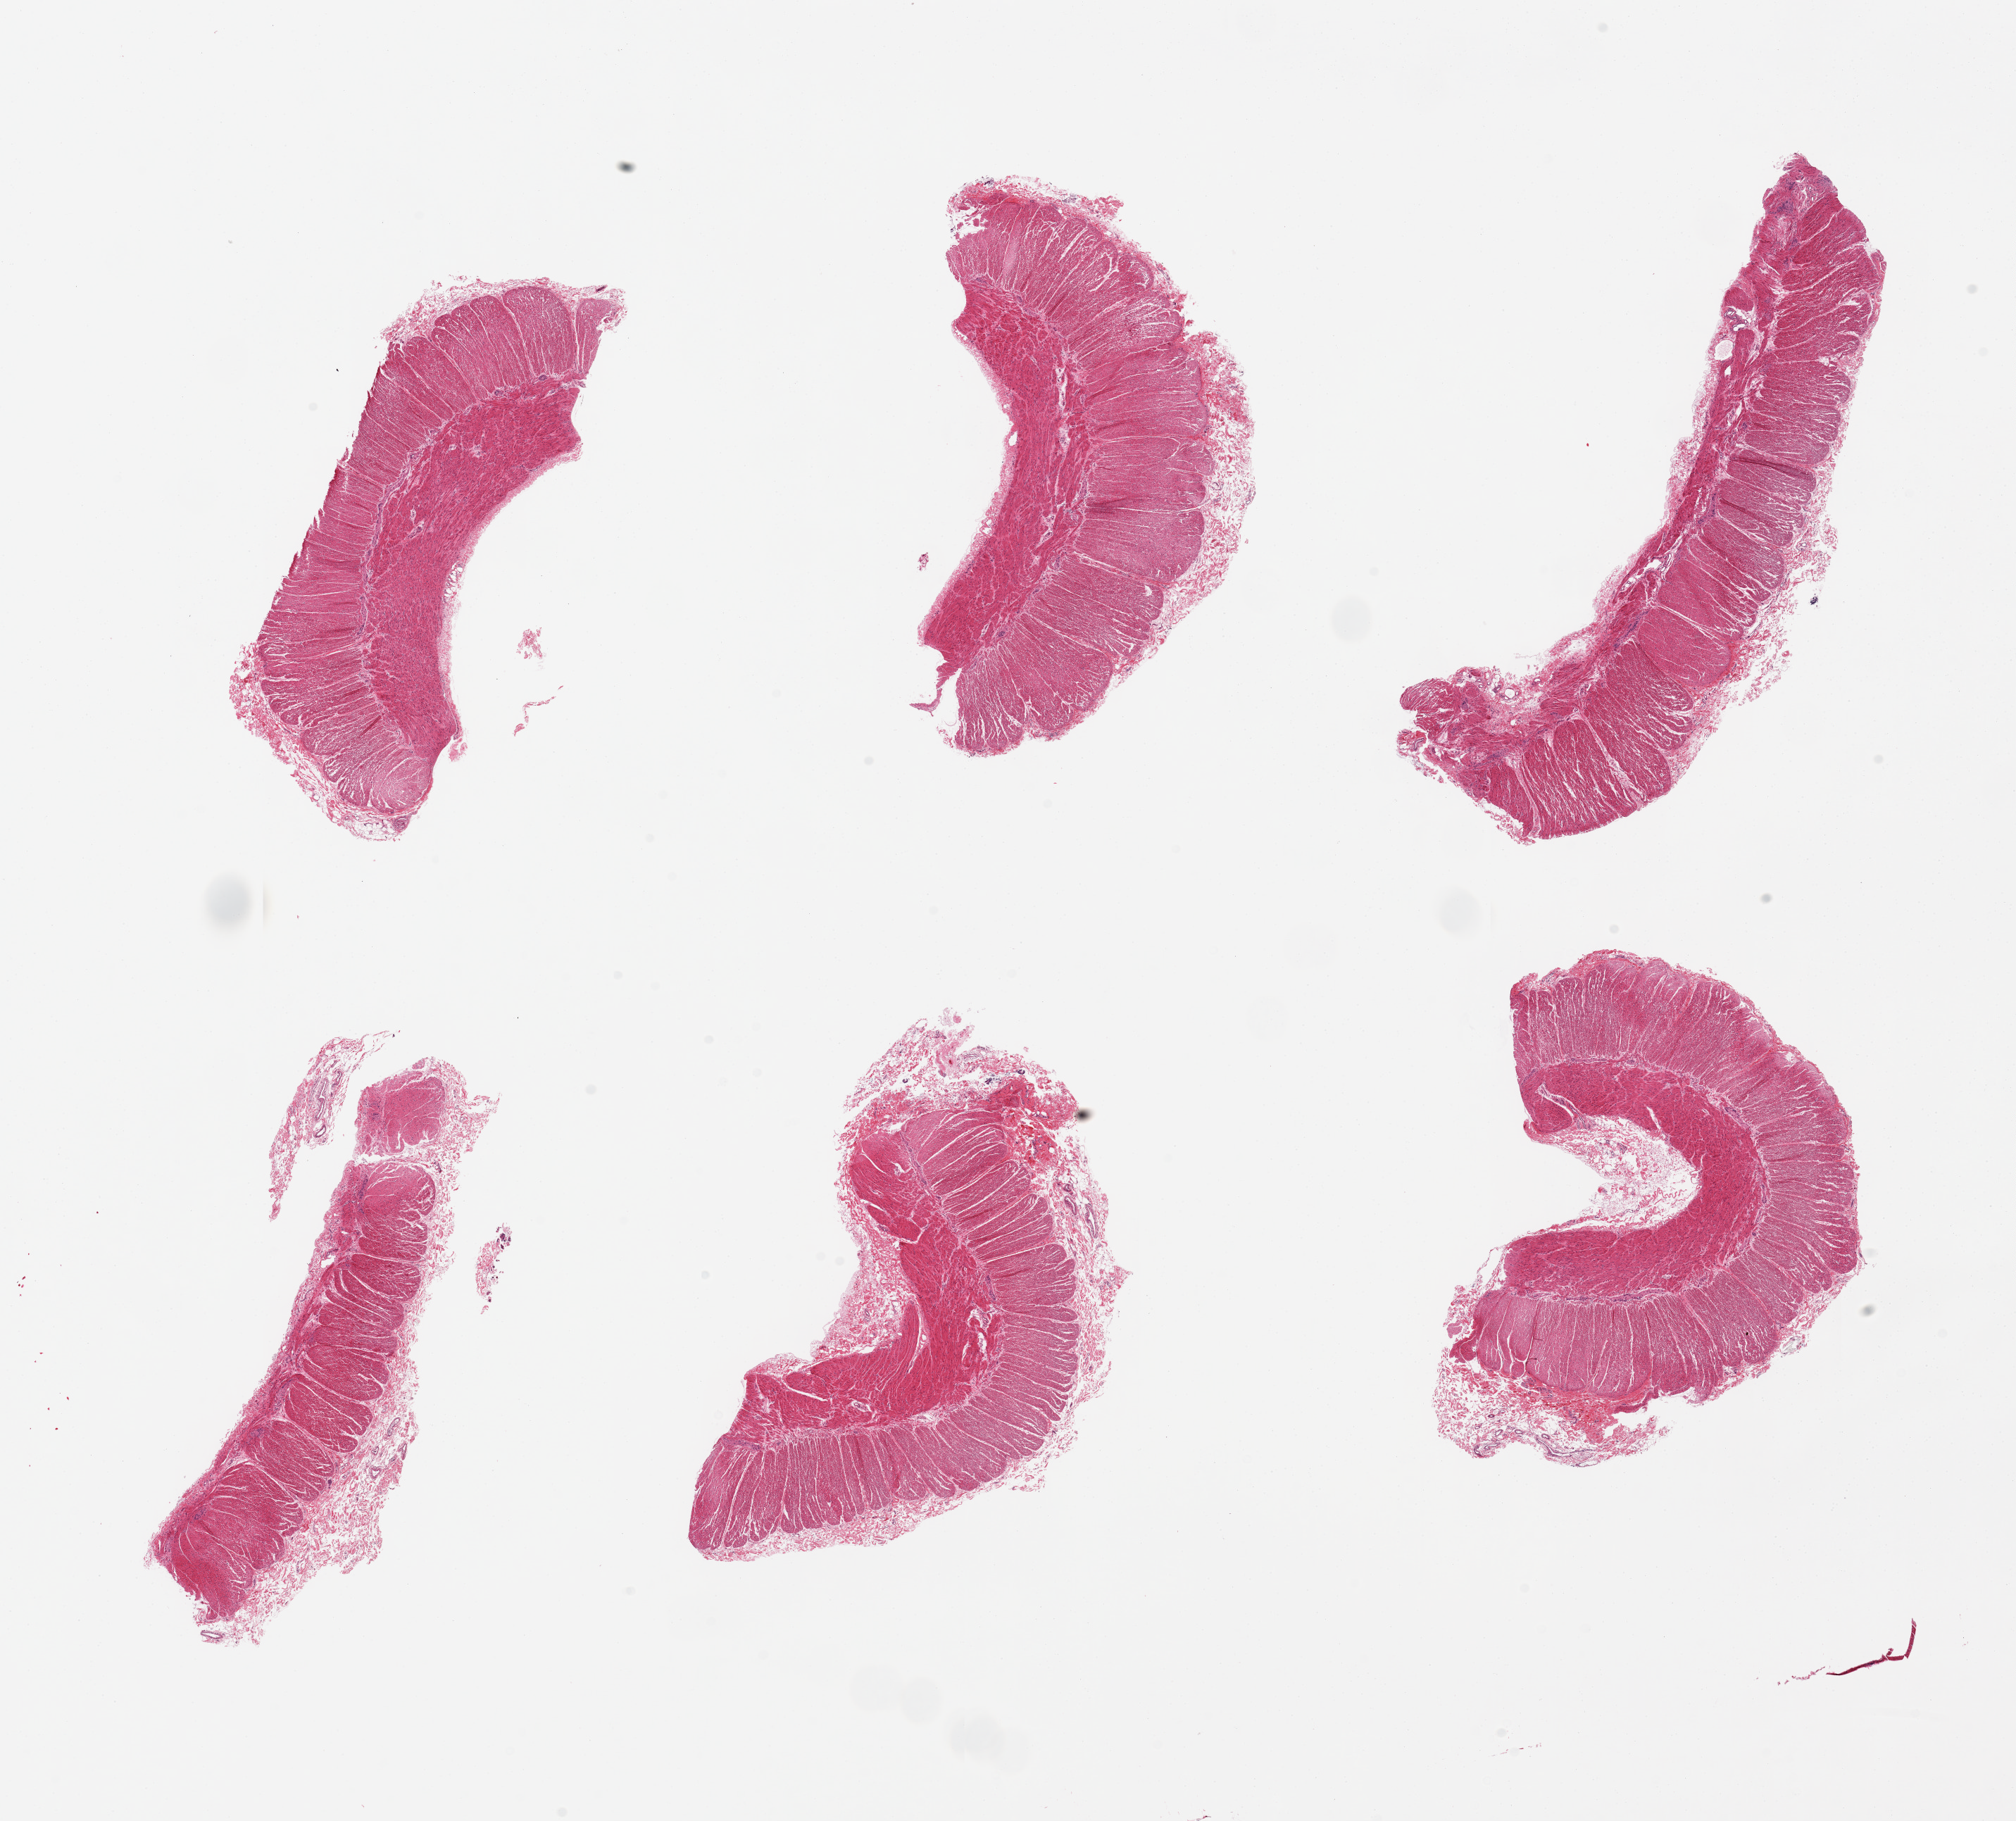
H&E whole-slide image, whole scanned area (about 22.6 x 20.5 mm, from a 20x scan) shown as a low-resolution overview. PAXgene-fixed, paraffin-embedded tissue. Sampled site (target tissue): transverse colon. Donor tissue sample.
Pathologist's review note for this sample: 1 piece, 7x2mm; all muscularis; no mucosa.